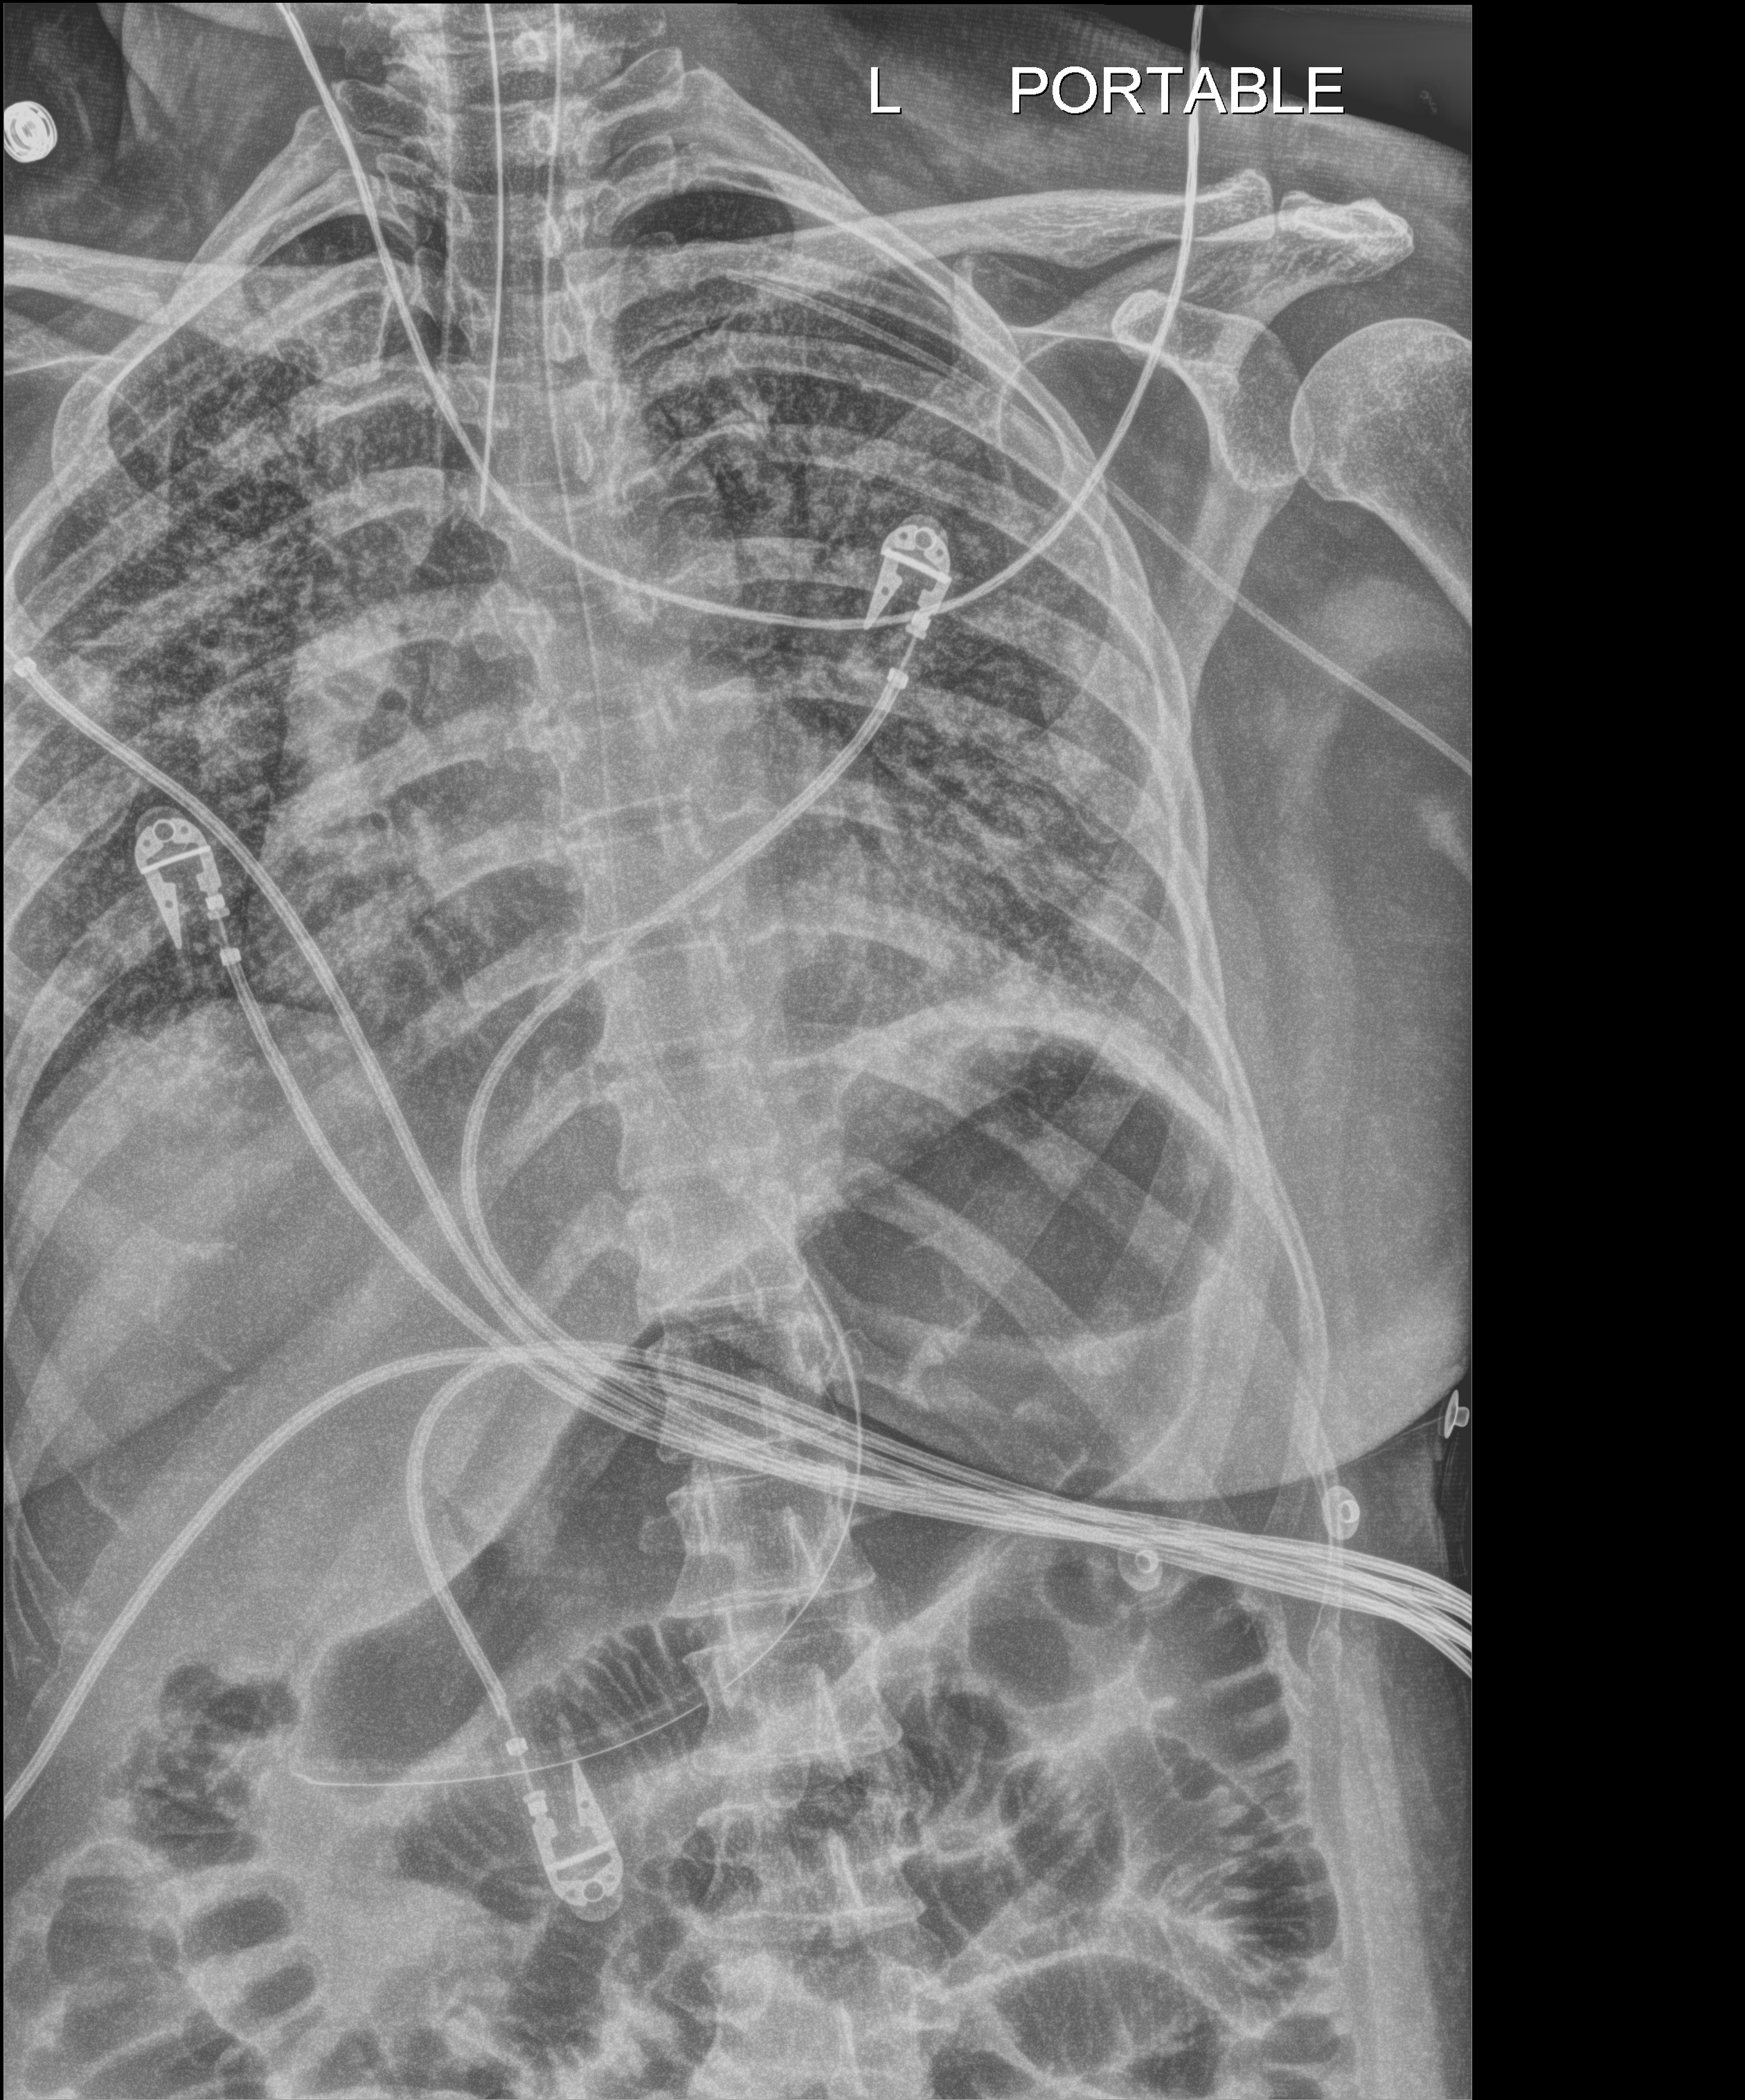
Chest X-ray (portable). Patient hospitalised with COVID-19; male, aged 18–59 years.
From the hospital-stay record, not from the radiograph (when in the stay this image was taken is not recorded): admitted to intensive care during this hospital stay: yes; mechanically ventilated during this hospital stay: yes.